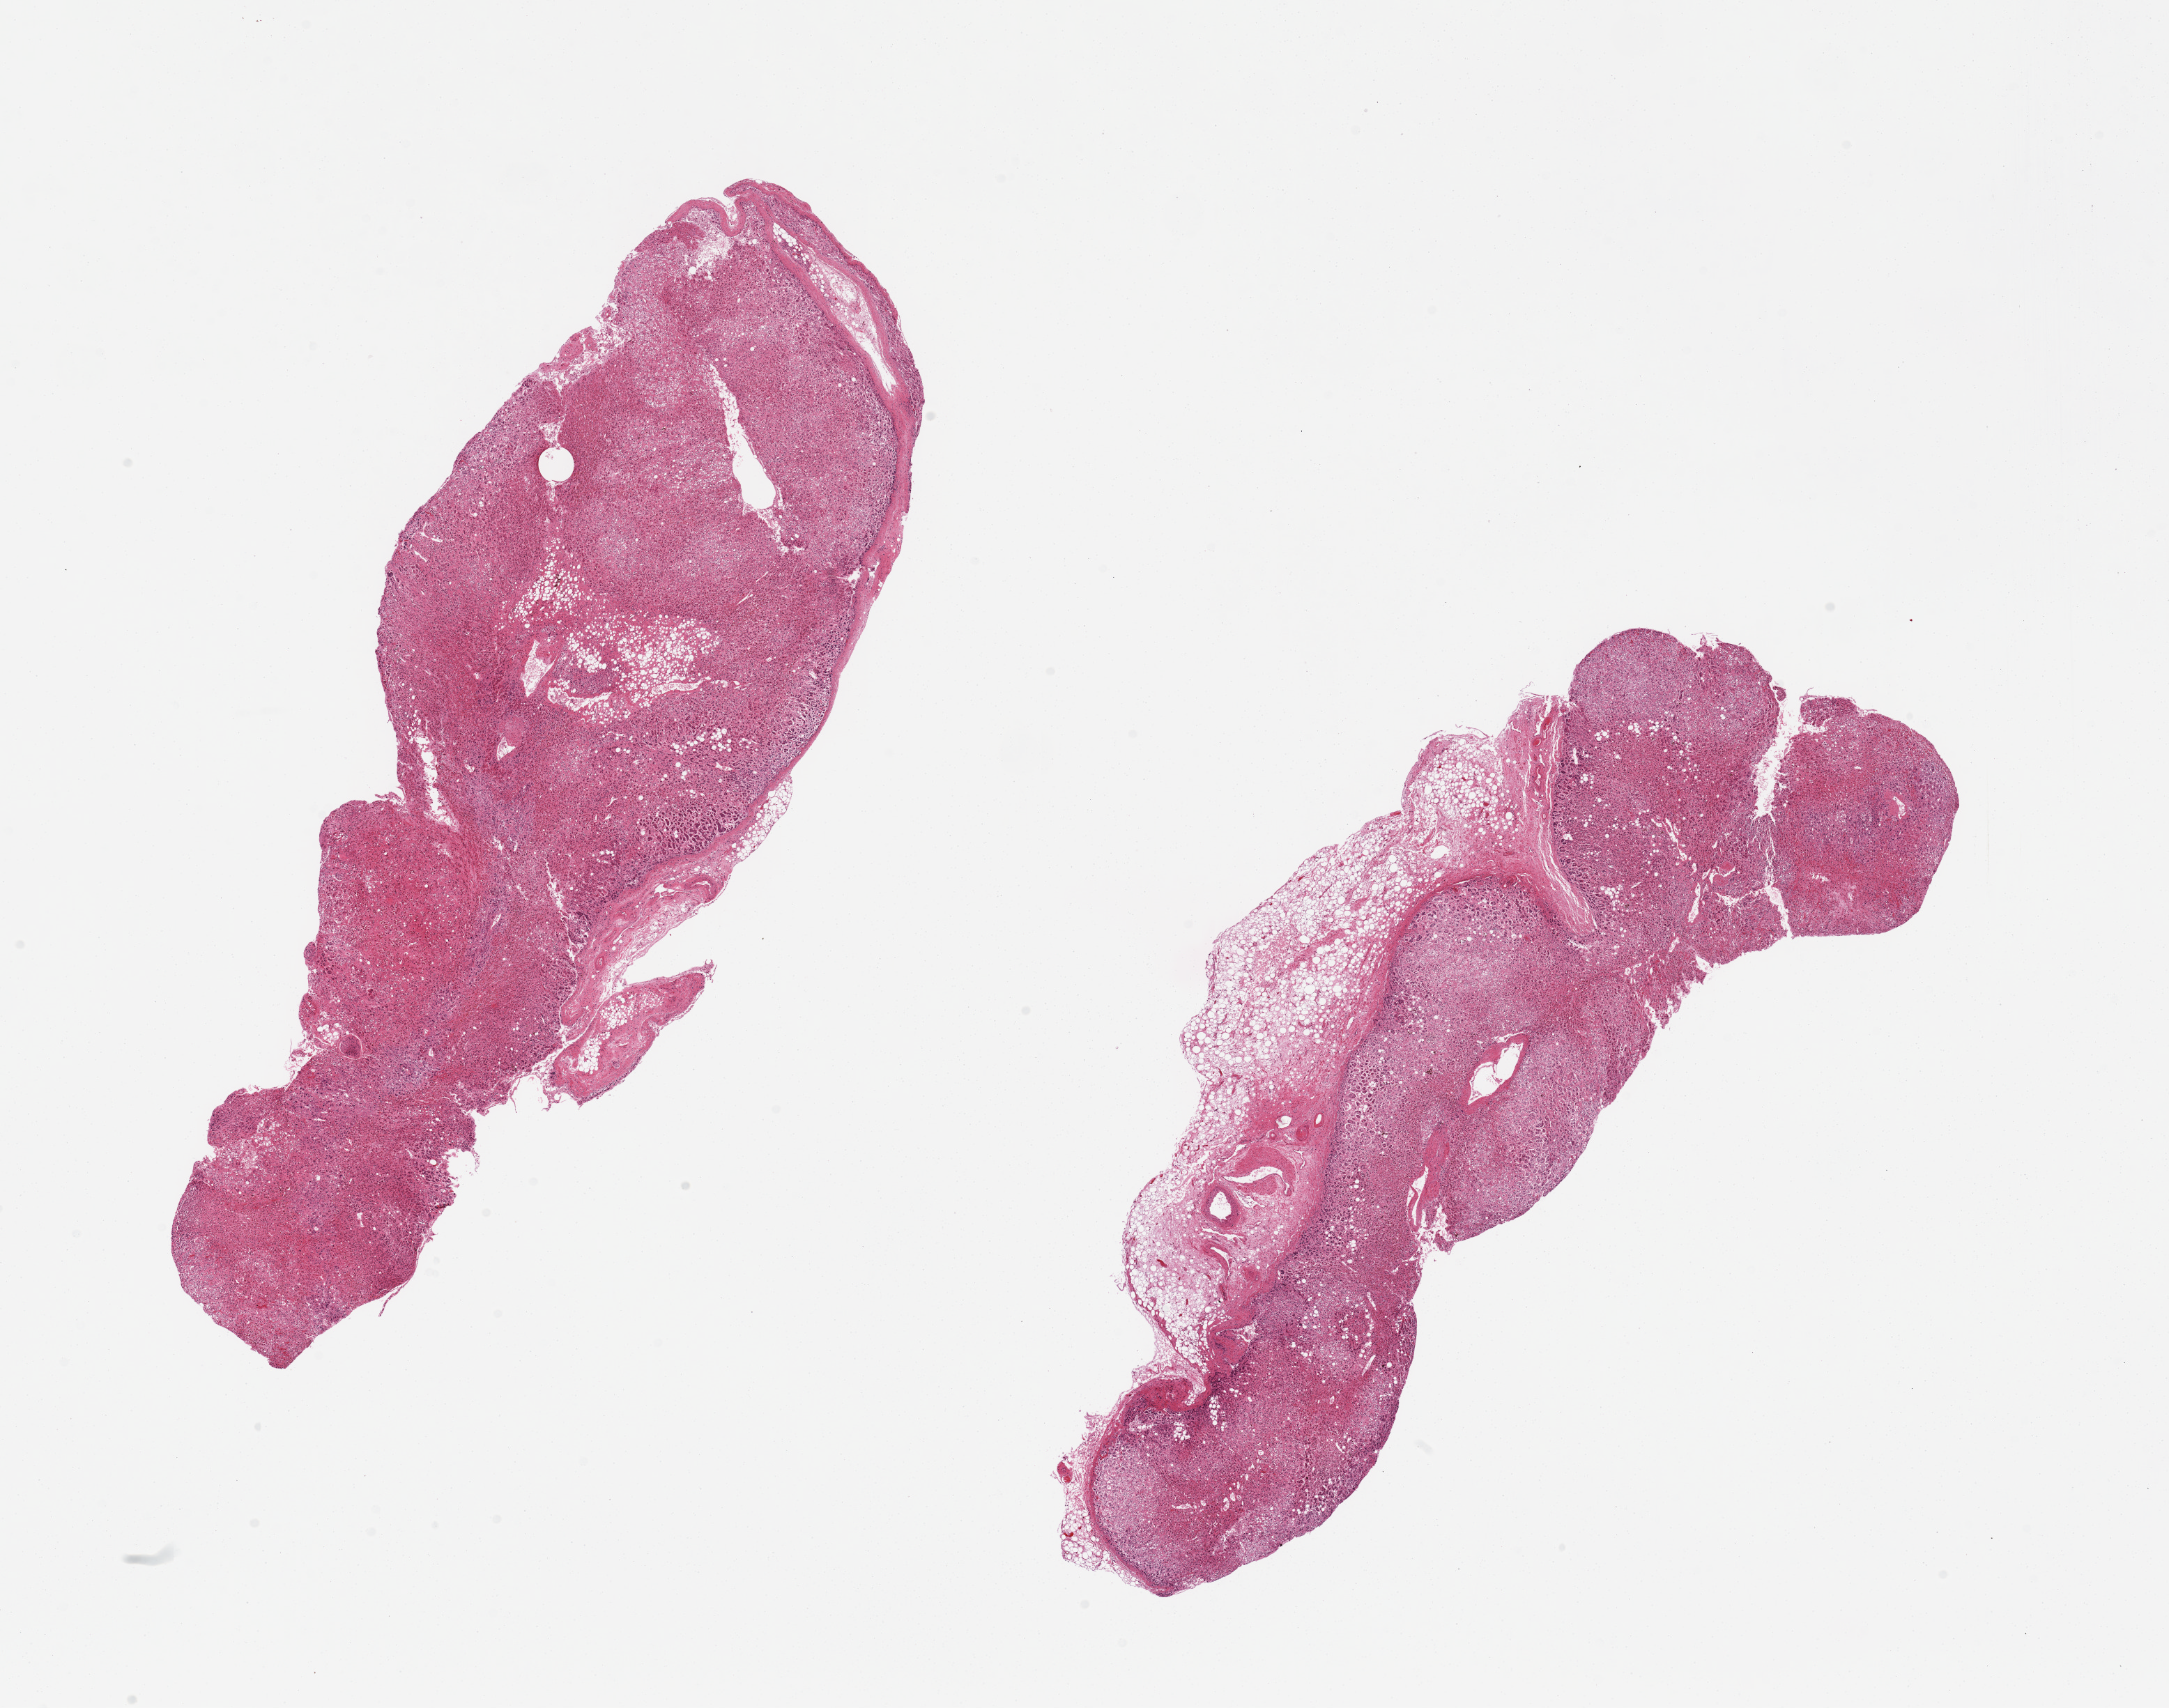
Digitized H&E-stained section, whole scanned area (about 24.6 x 19.4 mm, slide scanned at 20x) shown as a low-resolution overview; PAXgene-fixed paraffin-embedded (PFPE) section; section of adrenal gland (target tissue); donor tissue sample. Female donor.
Reviewer comment on this tissue sample: 2 pieces; 30% external fat.